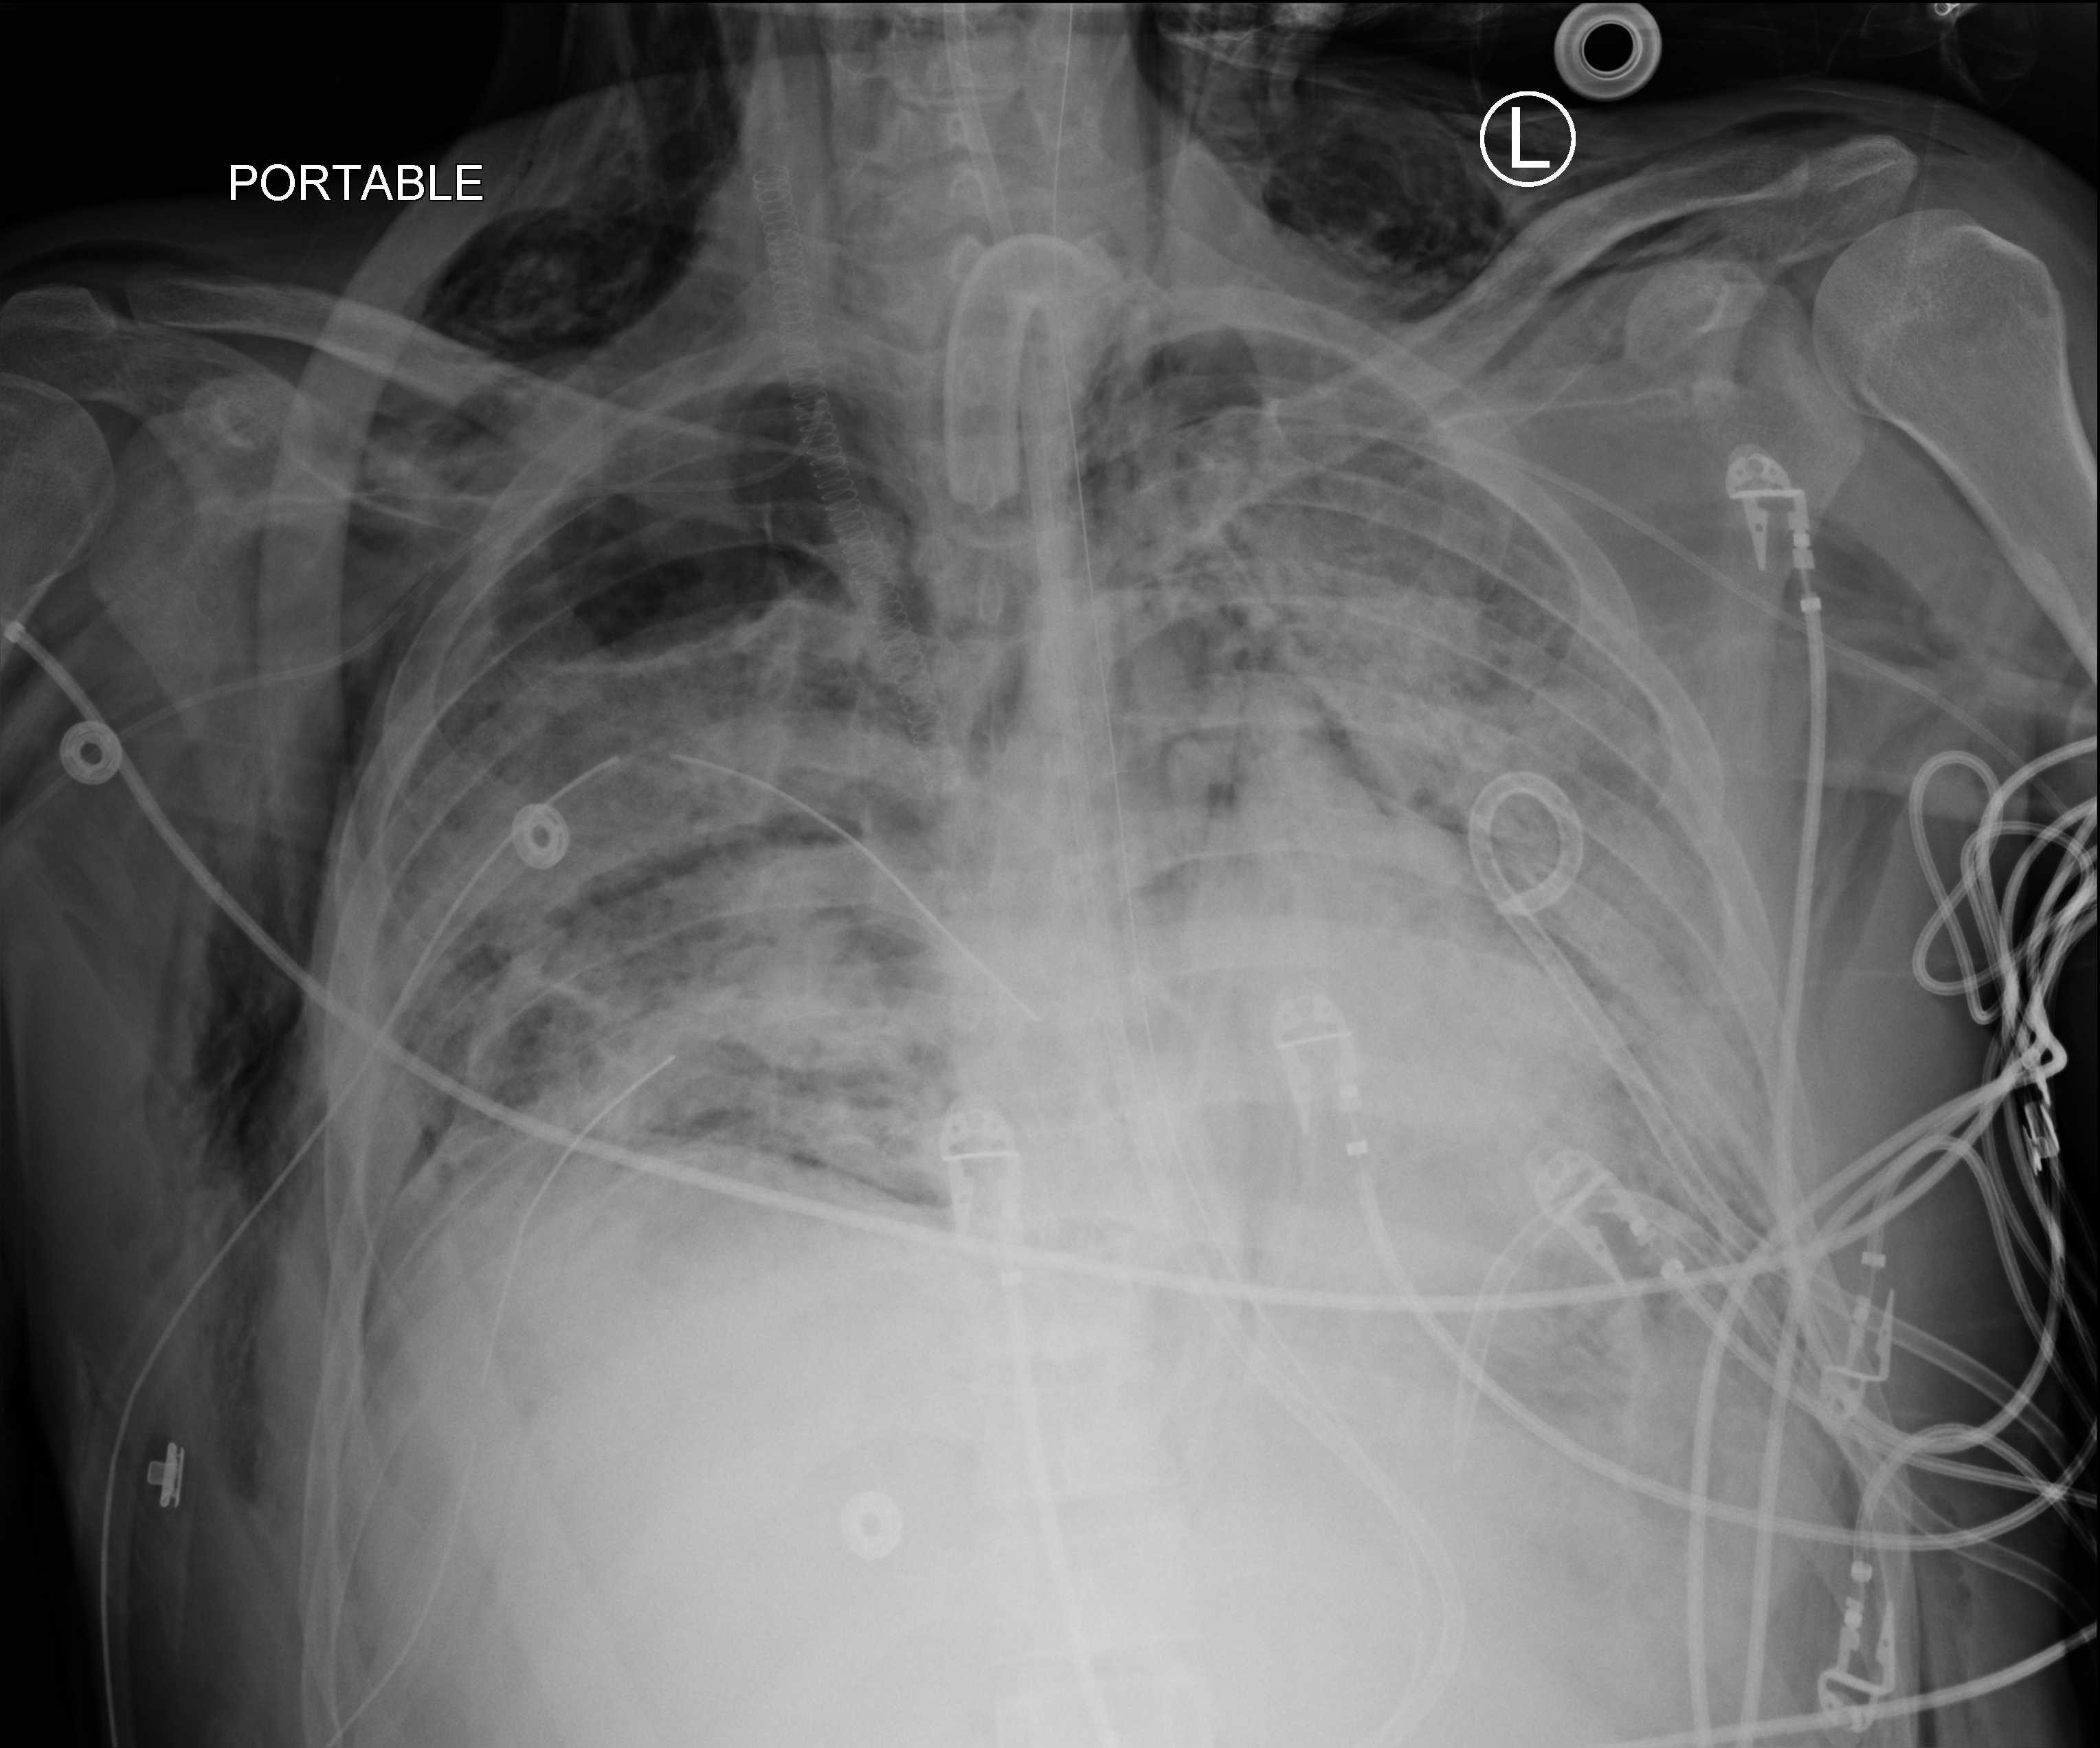
Chest X-ray (portable), anteroposterior (AP) projection. Adult patient hospitalised with COVID-19, age 18–59 years.
From the hospital-stay record, not from the radiograph (when in the stay this image was taken is not recorded): diabetes (admission record): no; other chronic lung disease (admission record): no; mechanically ventilated during this hospital stay: yes.